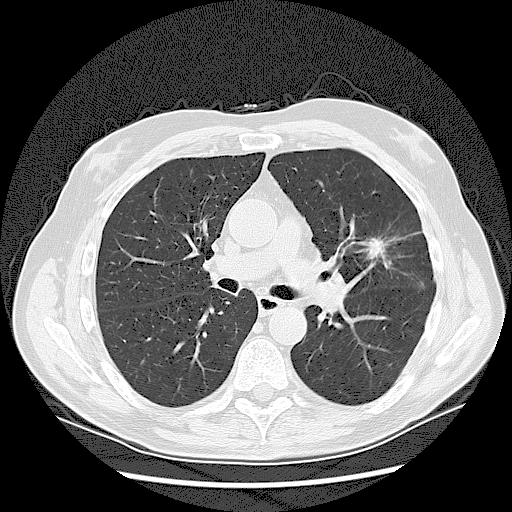
Chest CT (low-dose screening protocol), one axial image. Baseline screening round. Lung window (W 1500 / L -600 HU). 2.5 mm slice thickness. Lung (sharp) reconstruction kernel (LUNG). 120 kVp. 512 × 512 image matrix, field of view 380 × 380 mm. Male participant, aged 65 years at enrolment.
Lesion marked by an expert reader, bounding box (x1, y1, x2, y2) in pixels: (352, 229, 397, 272). Reader record for this screening exam (exam-level; its link to the box is not recorded): non-calcified nodule or mass ≥4 mm, left upper lobe, 37 × 27 mm, spiculated (stellate) margins, soft tissue attenuation. Official screen result: positive, change unspecified: nodule(s) >= 4 mm or enlarging nodule(s), mass(es), or other non-specific abnormalities suspicious for lung cancer. Participant outcome: lung cancer diagnosed 56 days after this screen — non-small cell carcinoma, poorly differentiated (G3), stage IA (AJCC 6th edition).